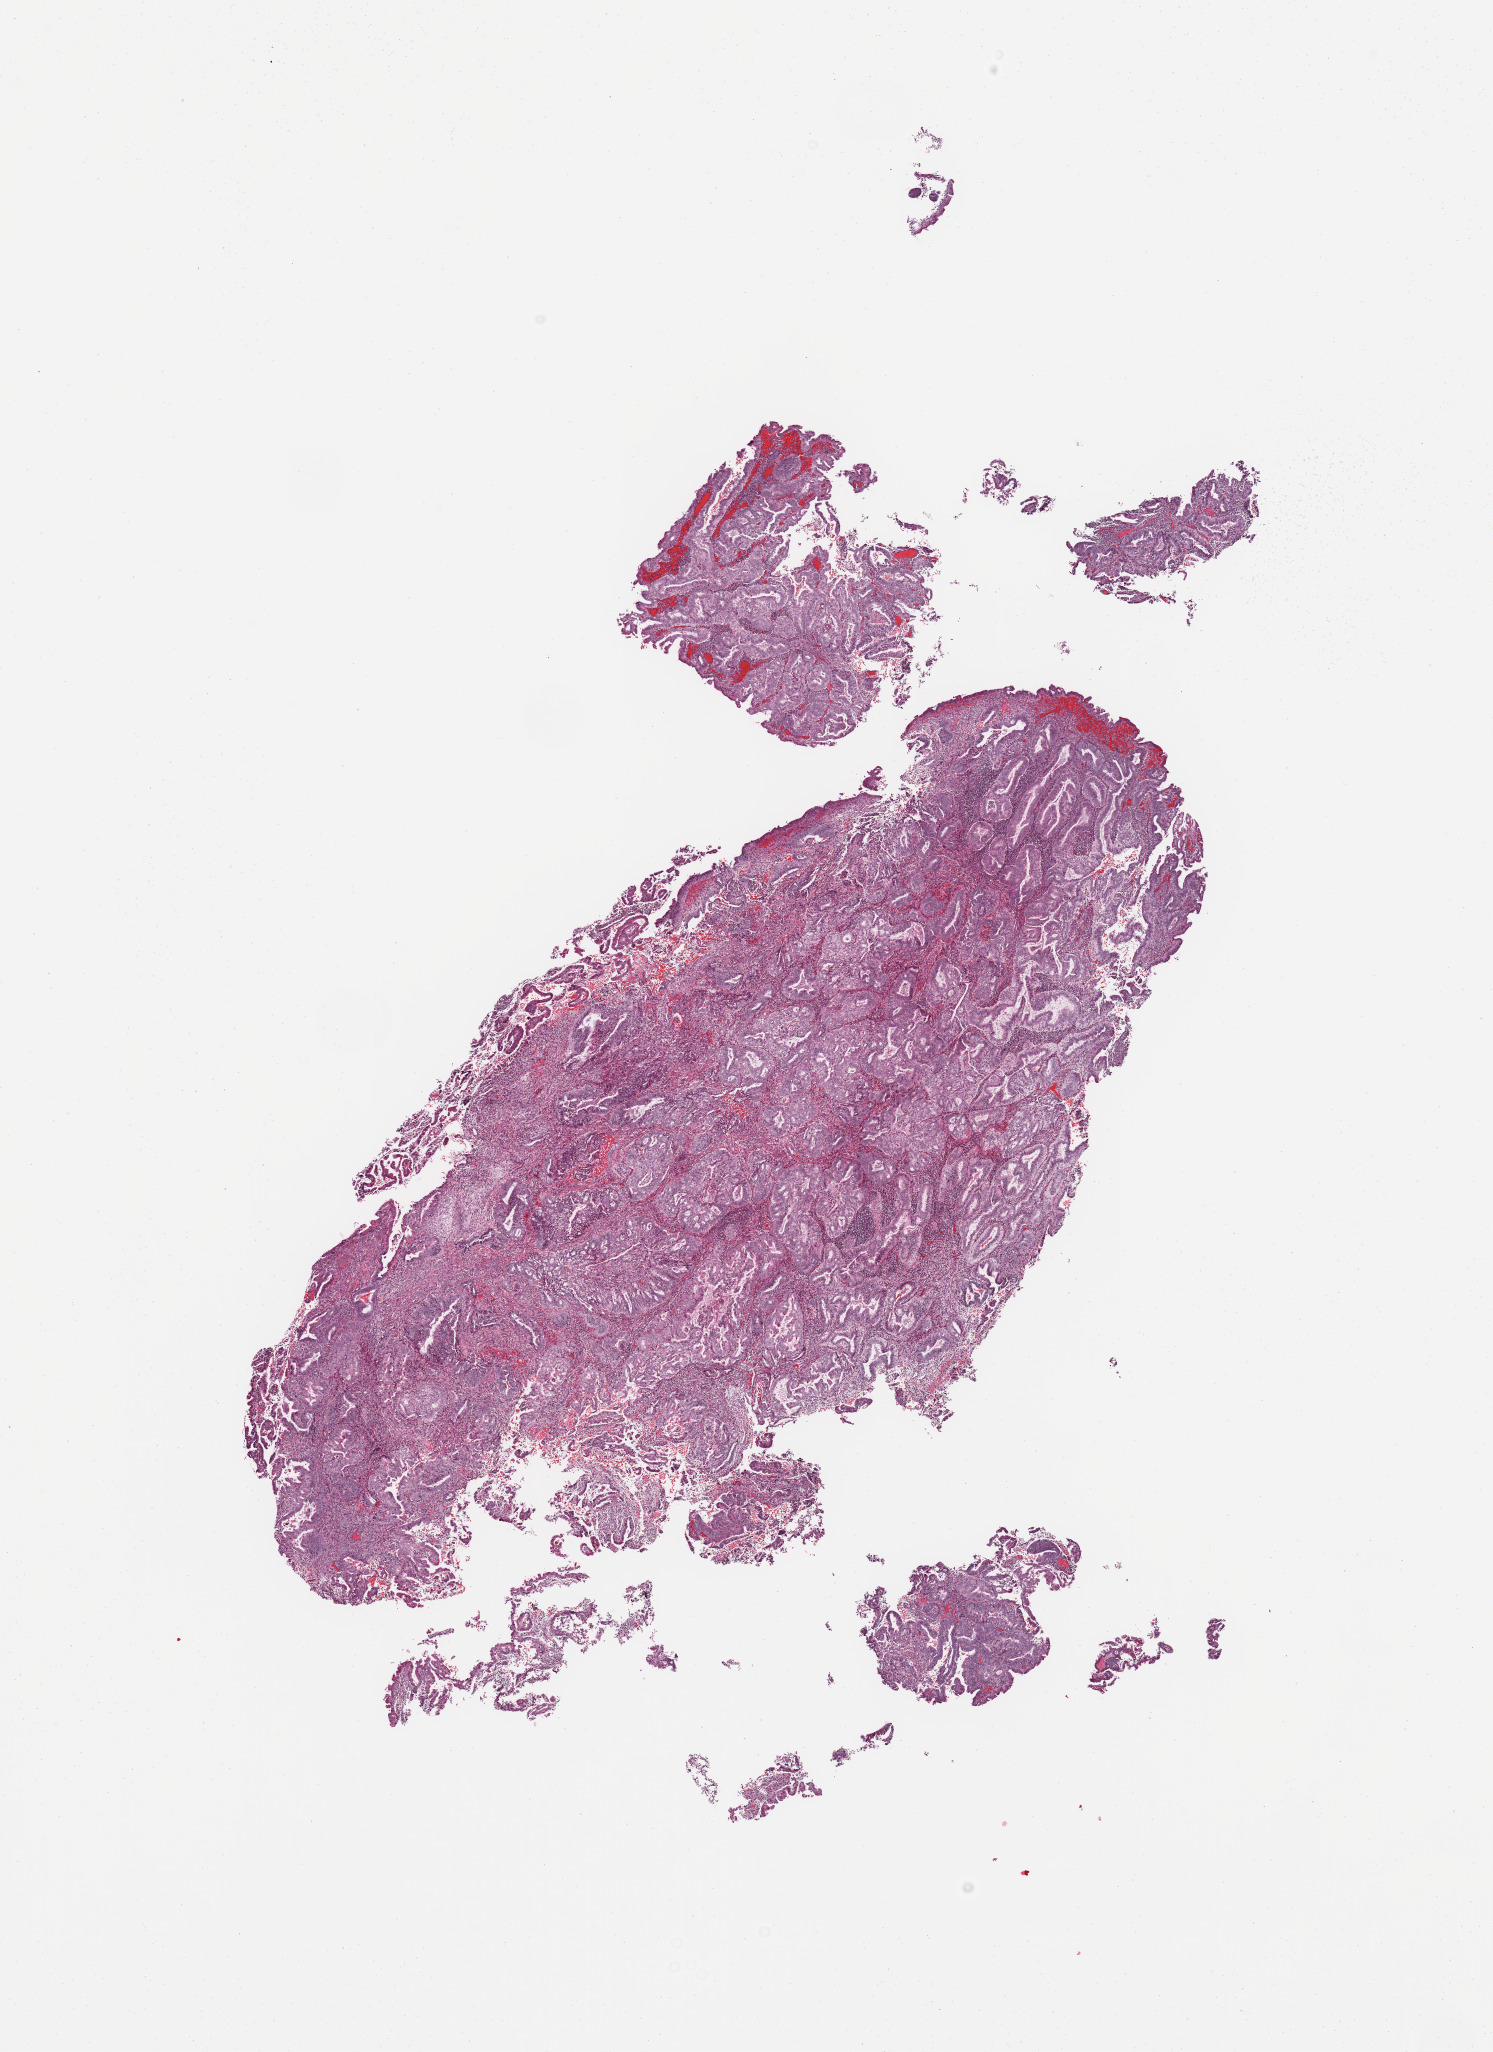
H&E whole-slide image, a low-resolution overview of the entire scanned area, about 11.8 x 16.2 mm (from a 20x scan); tumour tissue sample, uterus. Female, 56 y/o.
AJCC pathologic stage: I. Histologic diagnosis: Endometrioid adenocarcinoma, NOS.